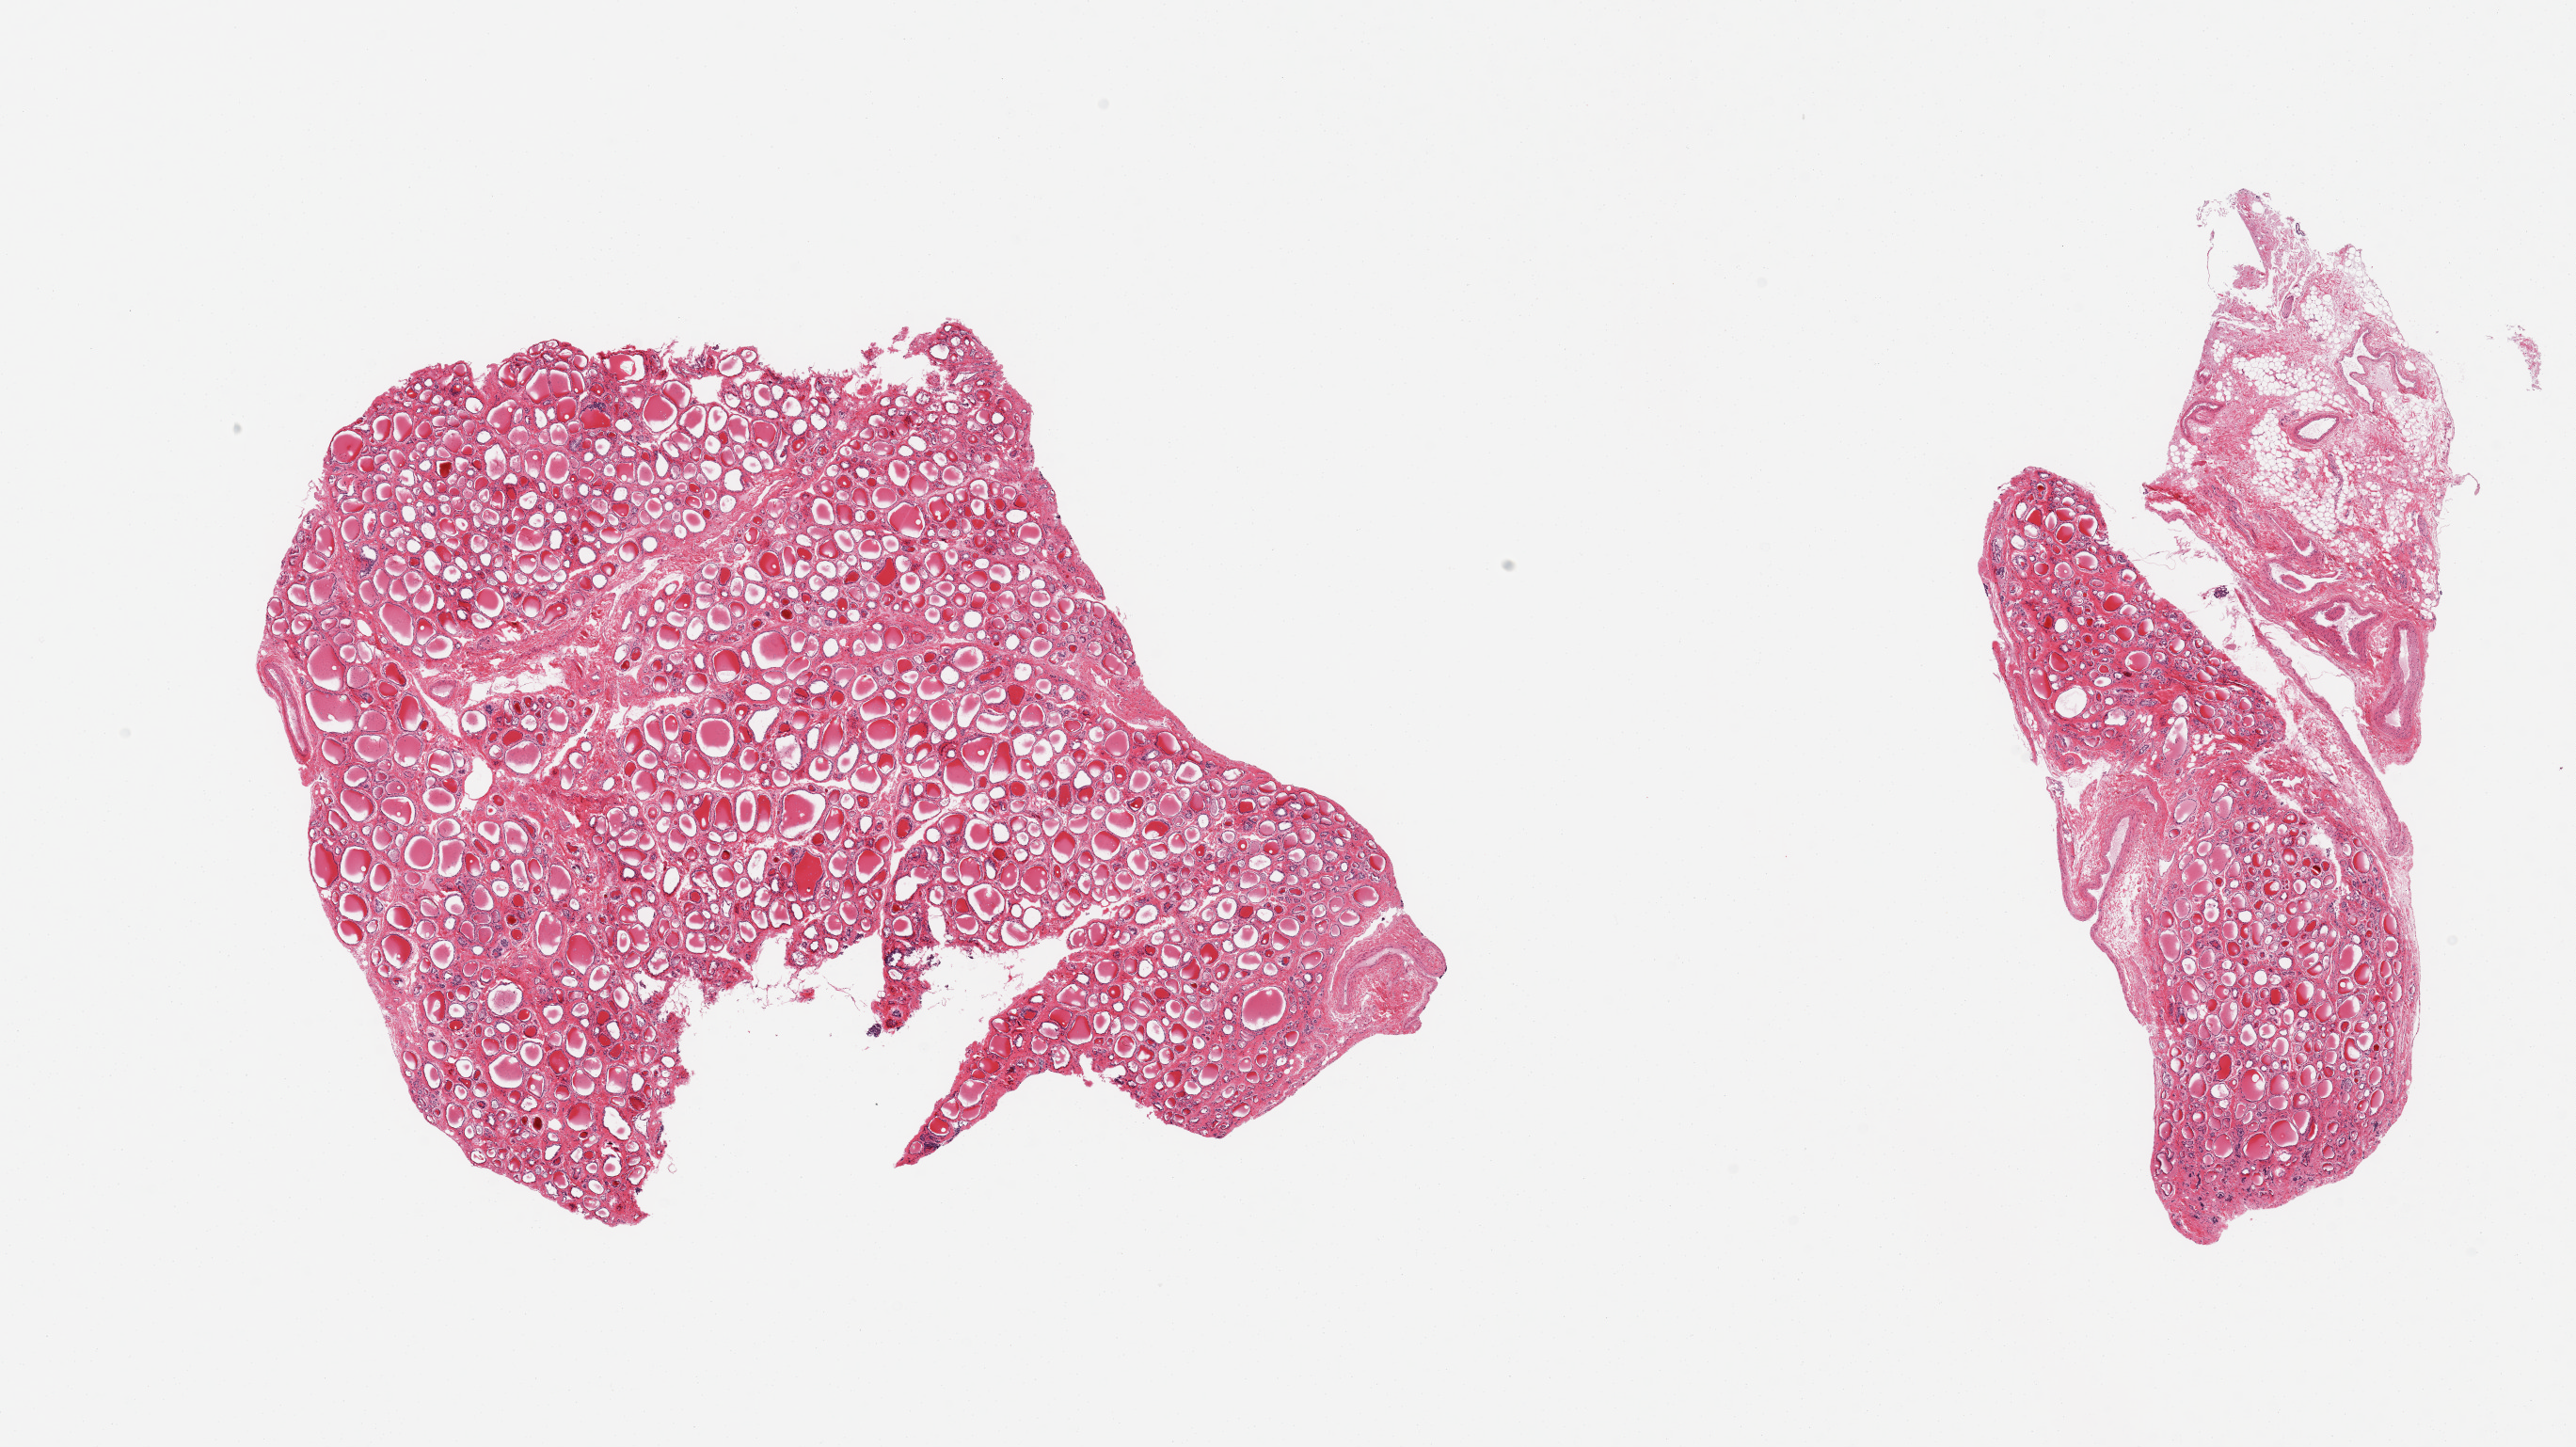
Whole-slide image, H&E stain — whole scanned area (about 21.7 x 12.2 mm, acquisition: 20x scan) shown as a low-resolution overview, PAXgene-fixed paraffin-embedded (PFPE) section, section of thyroid (target tissue), tissue donor sample.
Pathologist's review note for this sample: 2 pieces, no abnormalities; fragment of fibrofatty tissue.